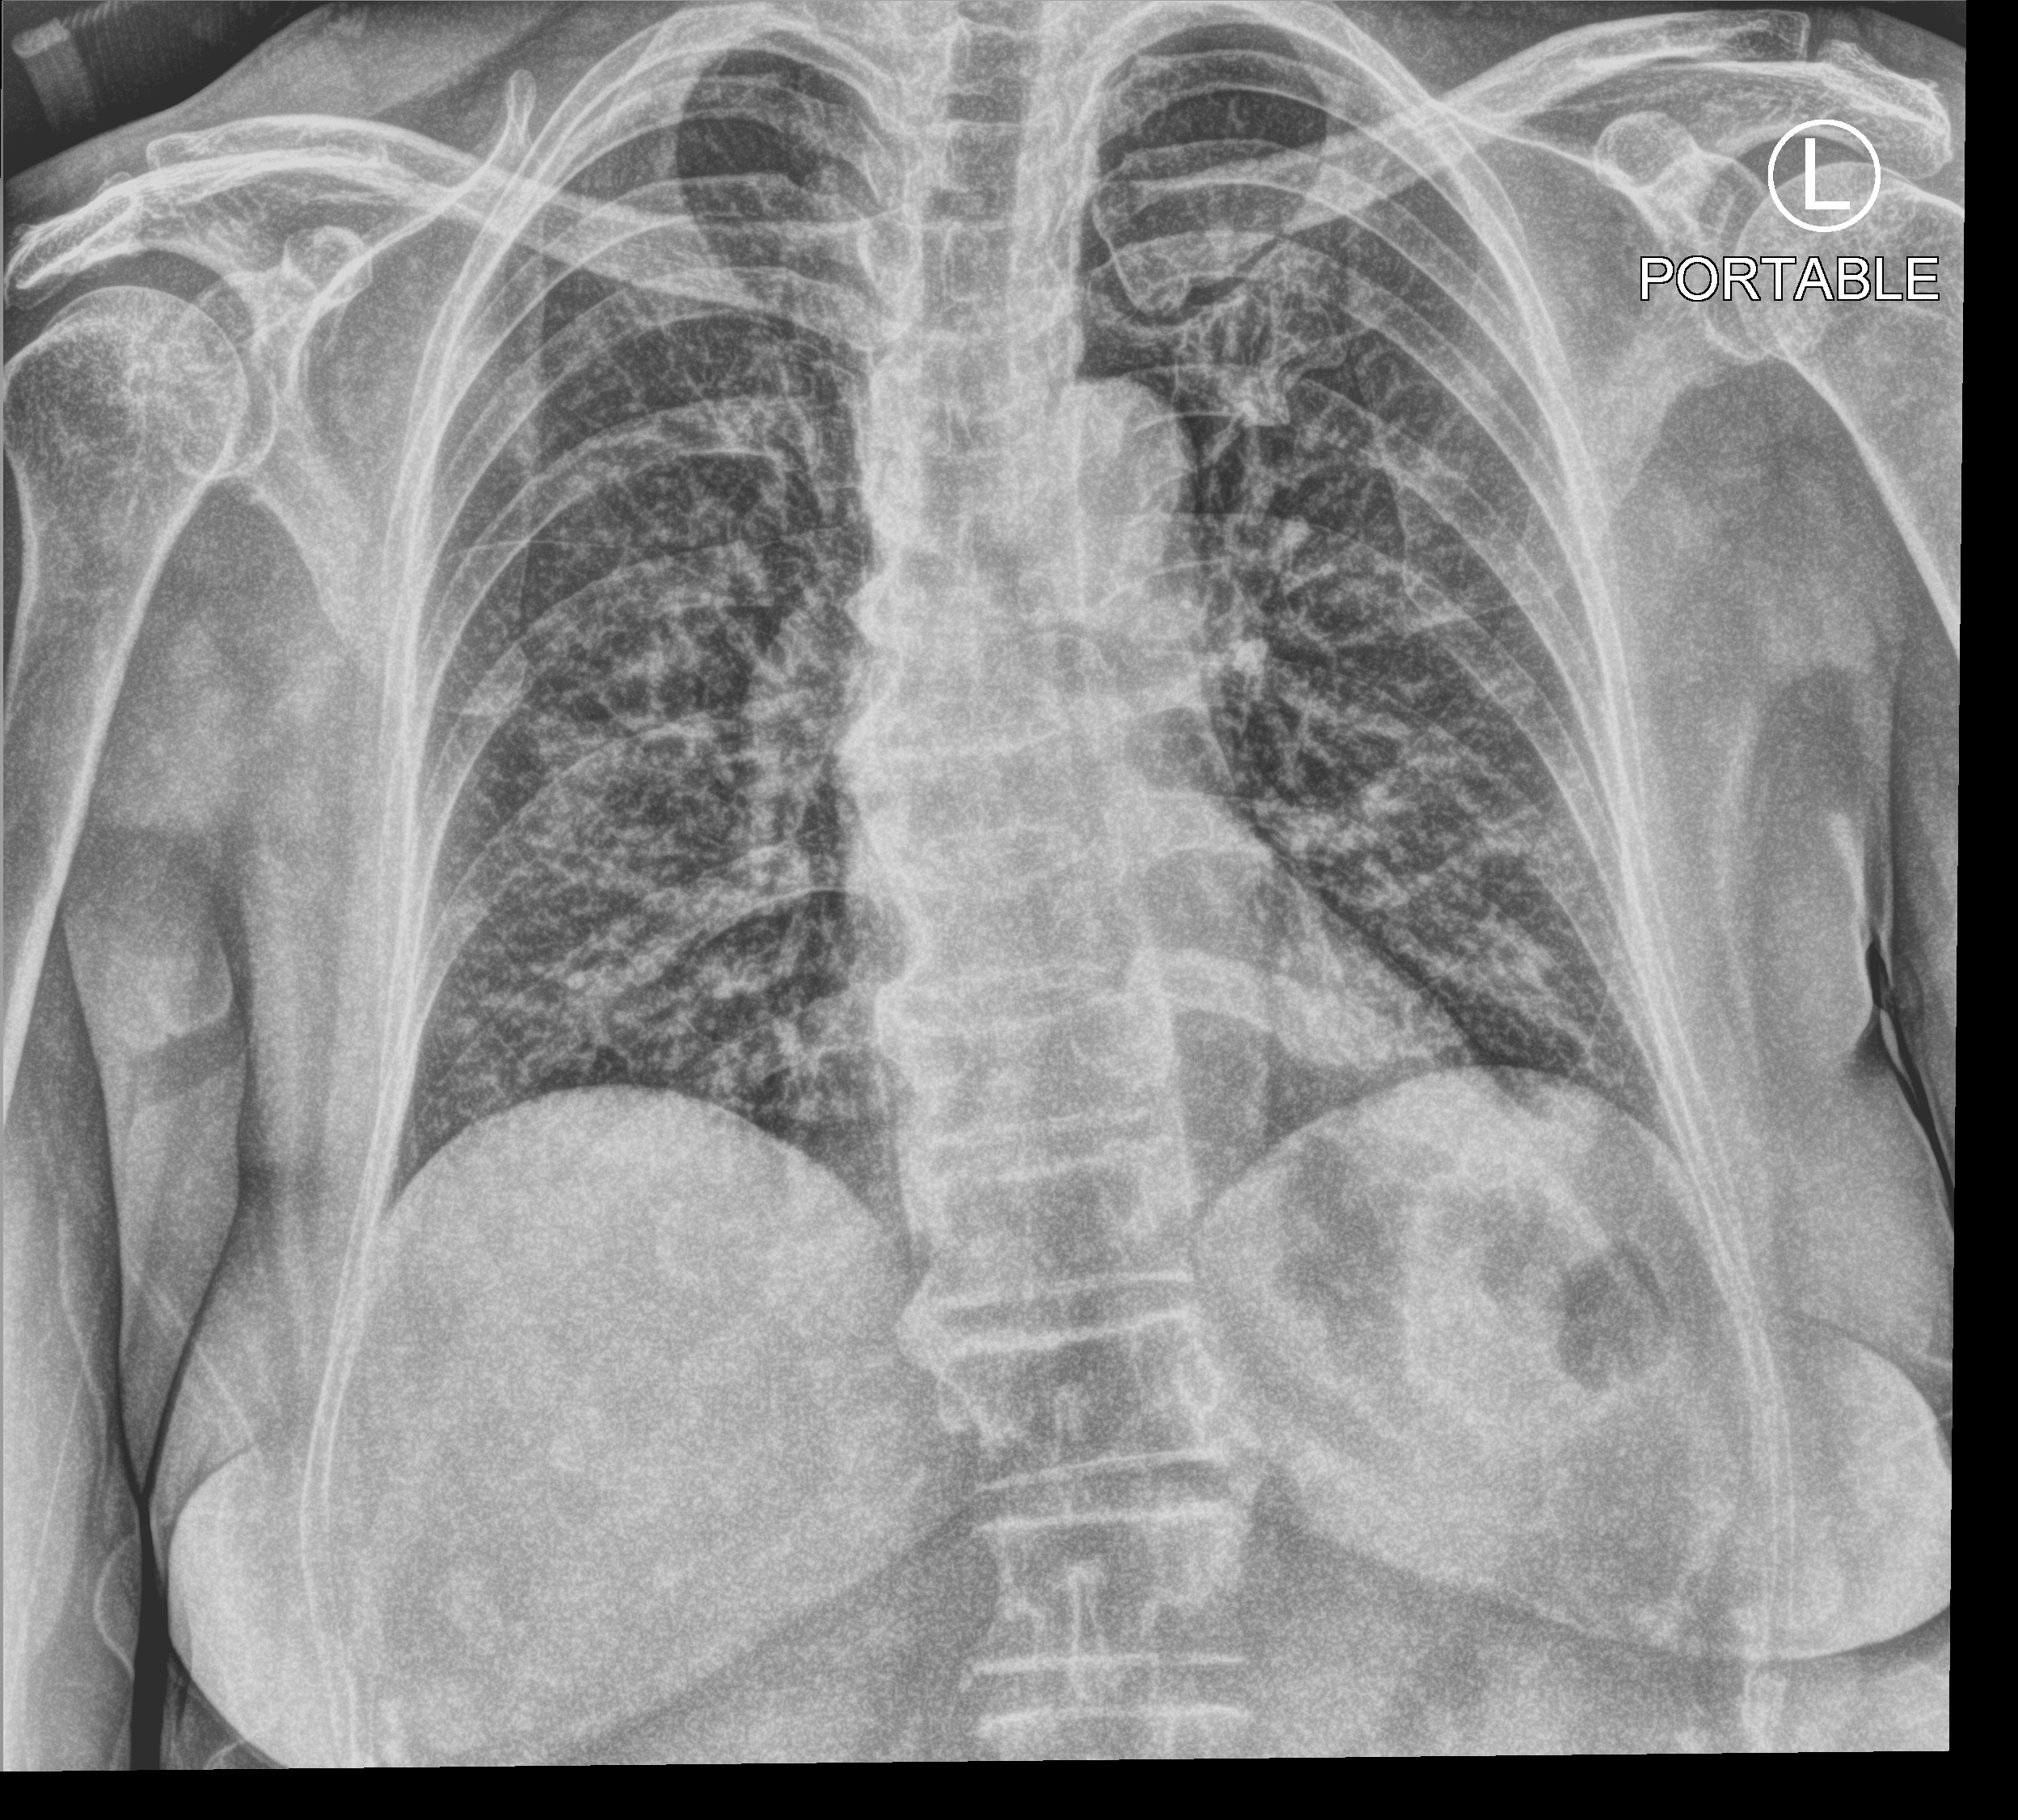
Chest X-ray (portable). Patient hospitalised with COVID-19; female, aged 60–74 years.
Hospital-stay facts (about this admission, not read from this image; timing relative to this image not recorded):
- chronic kidney disease (admission record): no